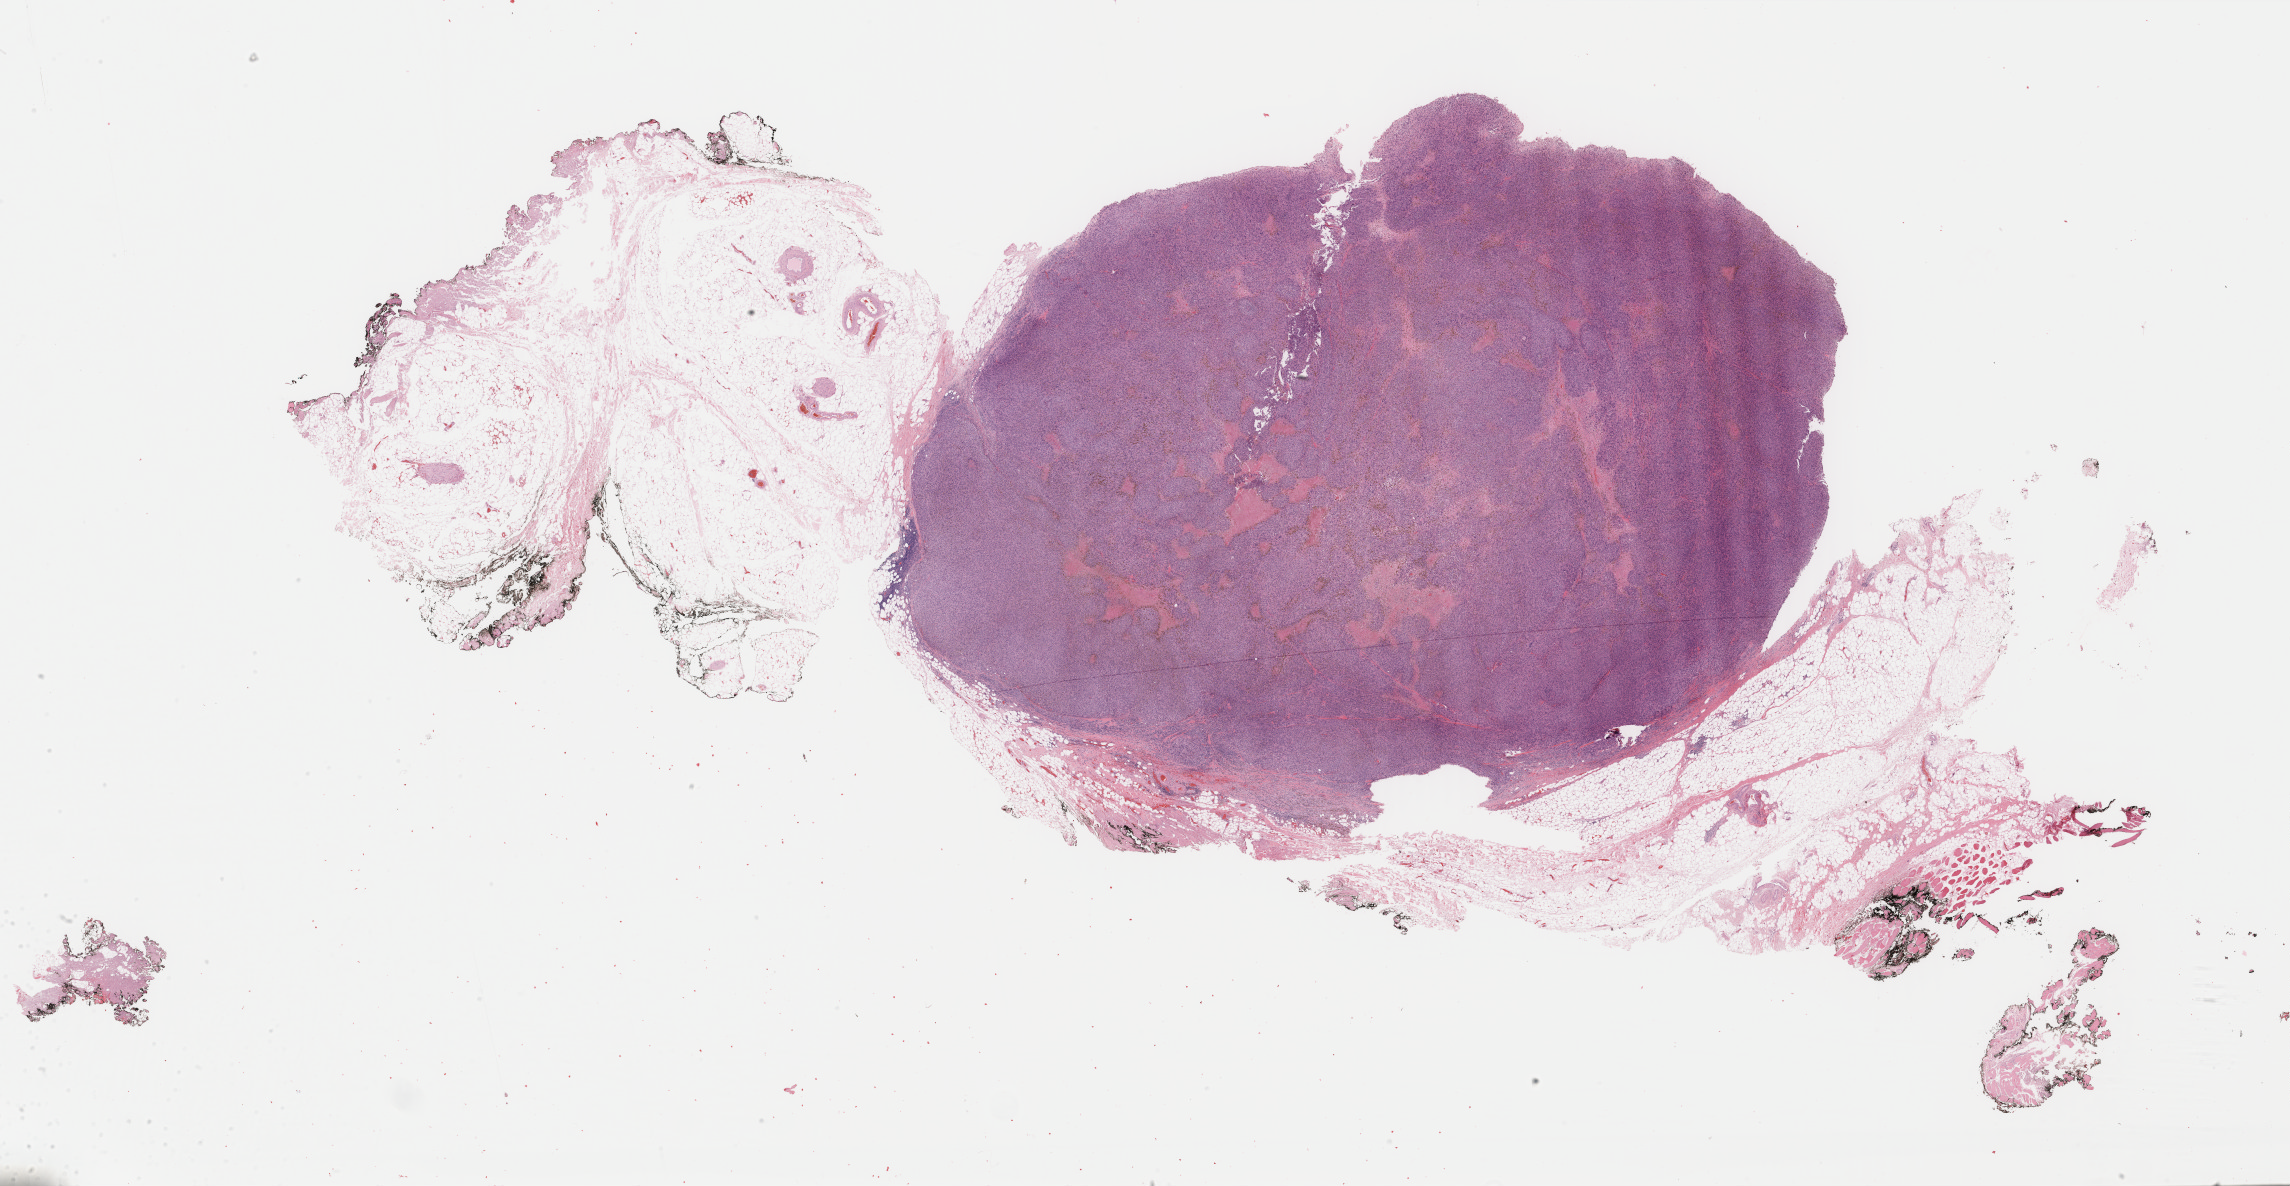
Digitized H&E-stained tissue section (whole slide) — a low-resolution overview of the entire scanned area, about 36.4 x 18.8 mm; formalin-fixed paraffin-embedded (FFPE) diagnostic section; sample: primary tumour, skin. Male, age 62 years at initial diagnosis.
Pathologic diagnosis: Malignant melanoma, NOS. TNM: T3b N0 M0. AJCC pathologic stage: IIB (6th edition).